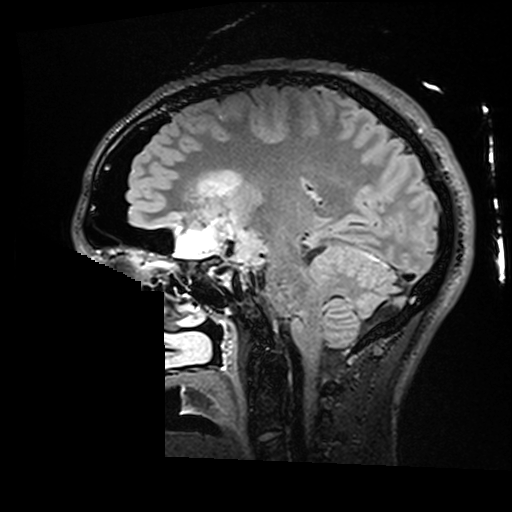
Brain MRI from a brain-tumour surgery series, one sagittal slice. Position 99 of 176 along the scan axis. T2 FLAIR. 1 mm slice thickness. 512 × 512 image matrix, field of view 250 × 250 mm. Case-level facts recorded for this patient, not image findings: histopathology: Astrocytoma; WHO grade: 2; IDH mutation: yes; tumour location: Right Insular.
Structures marked on this image (outlined manually by an expert reader):
- residual tumour: bounding box (x1, y1, x2, y2) in pixels: (199, 171, 242, 197)